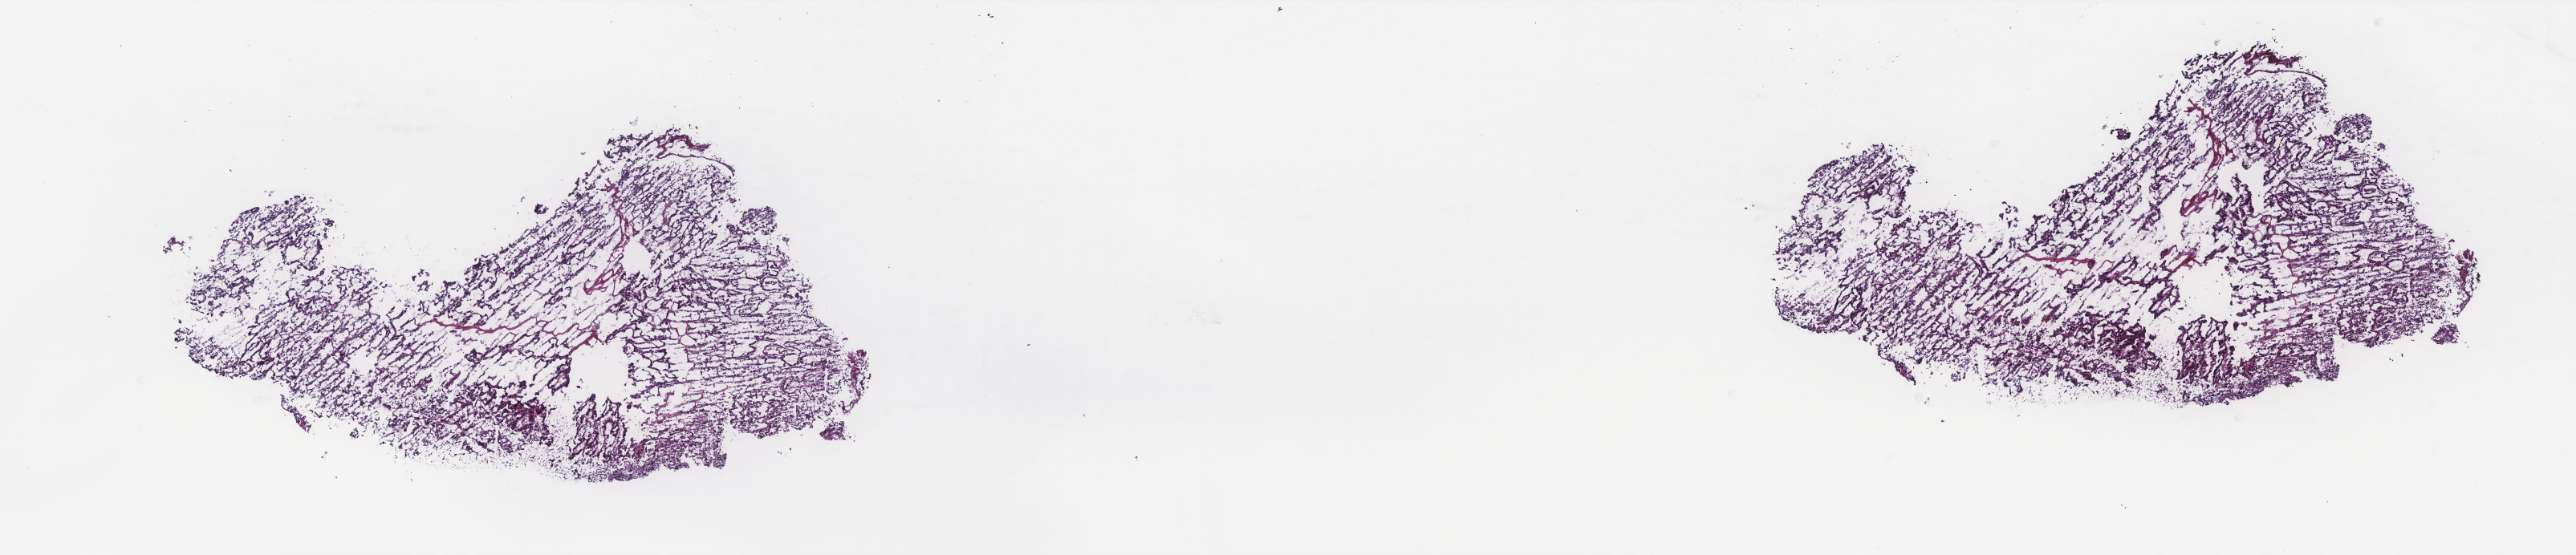
Whole-slide histology image, H&E, low-resolution overview of the scanned area, about 25.7 x 5.5 mm (from a 40x scan). Frozen section from the top of the tissue portion. Uterus, primary tumour sample. Female patient; age at initial diagnosis 59 years. Histologic grade: G3 (poorly differentiated). Slide review estimates, as recorded: tumour cells 85%, tumour nuclei 90%, normal cells 0%, stromal cells 10%, necrosis 5%. Infiltration values recorded for this section: lymphocyte infiltration 2%, monocyte infiltration 4%, neutrophil infiltration 2%.
FIGO stage: II. Histologic diagnosis: Endometrioid adenocarcinoma, NOS (endometrium).